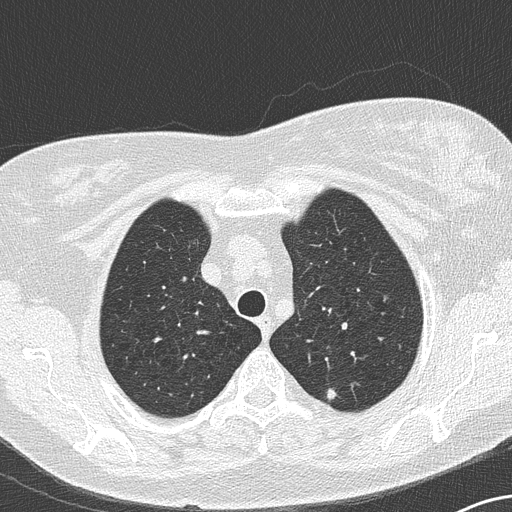
Chest CT (low-dose screening protocol), one axial image, second screening round (one year after baseline), lung window (W 1500 / L -600 HU), 2 mm slice thickness. Female participant, aged 65 years at enrolment.
Expert reader's lesion annotation, bounding box [x1, y1, x2, y2] px = [310, 379, 353, 414]. The exam's reader record, not a measurement of the box and not confirmed to be the same lesion: non-calcified nodule or mass ≥4 mm, left upper lobe, 7 × 6 mm, soft tissue attenuation, pre-existing on the prior screen: yes.